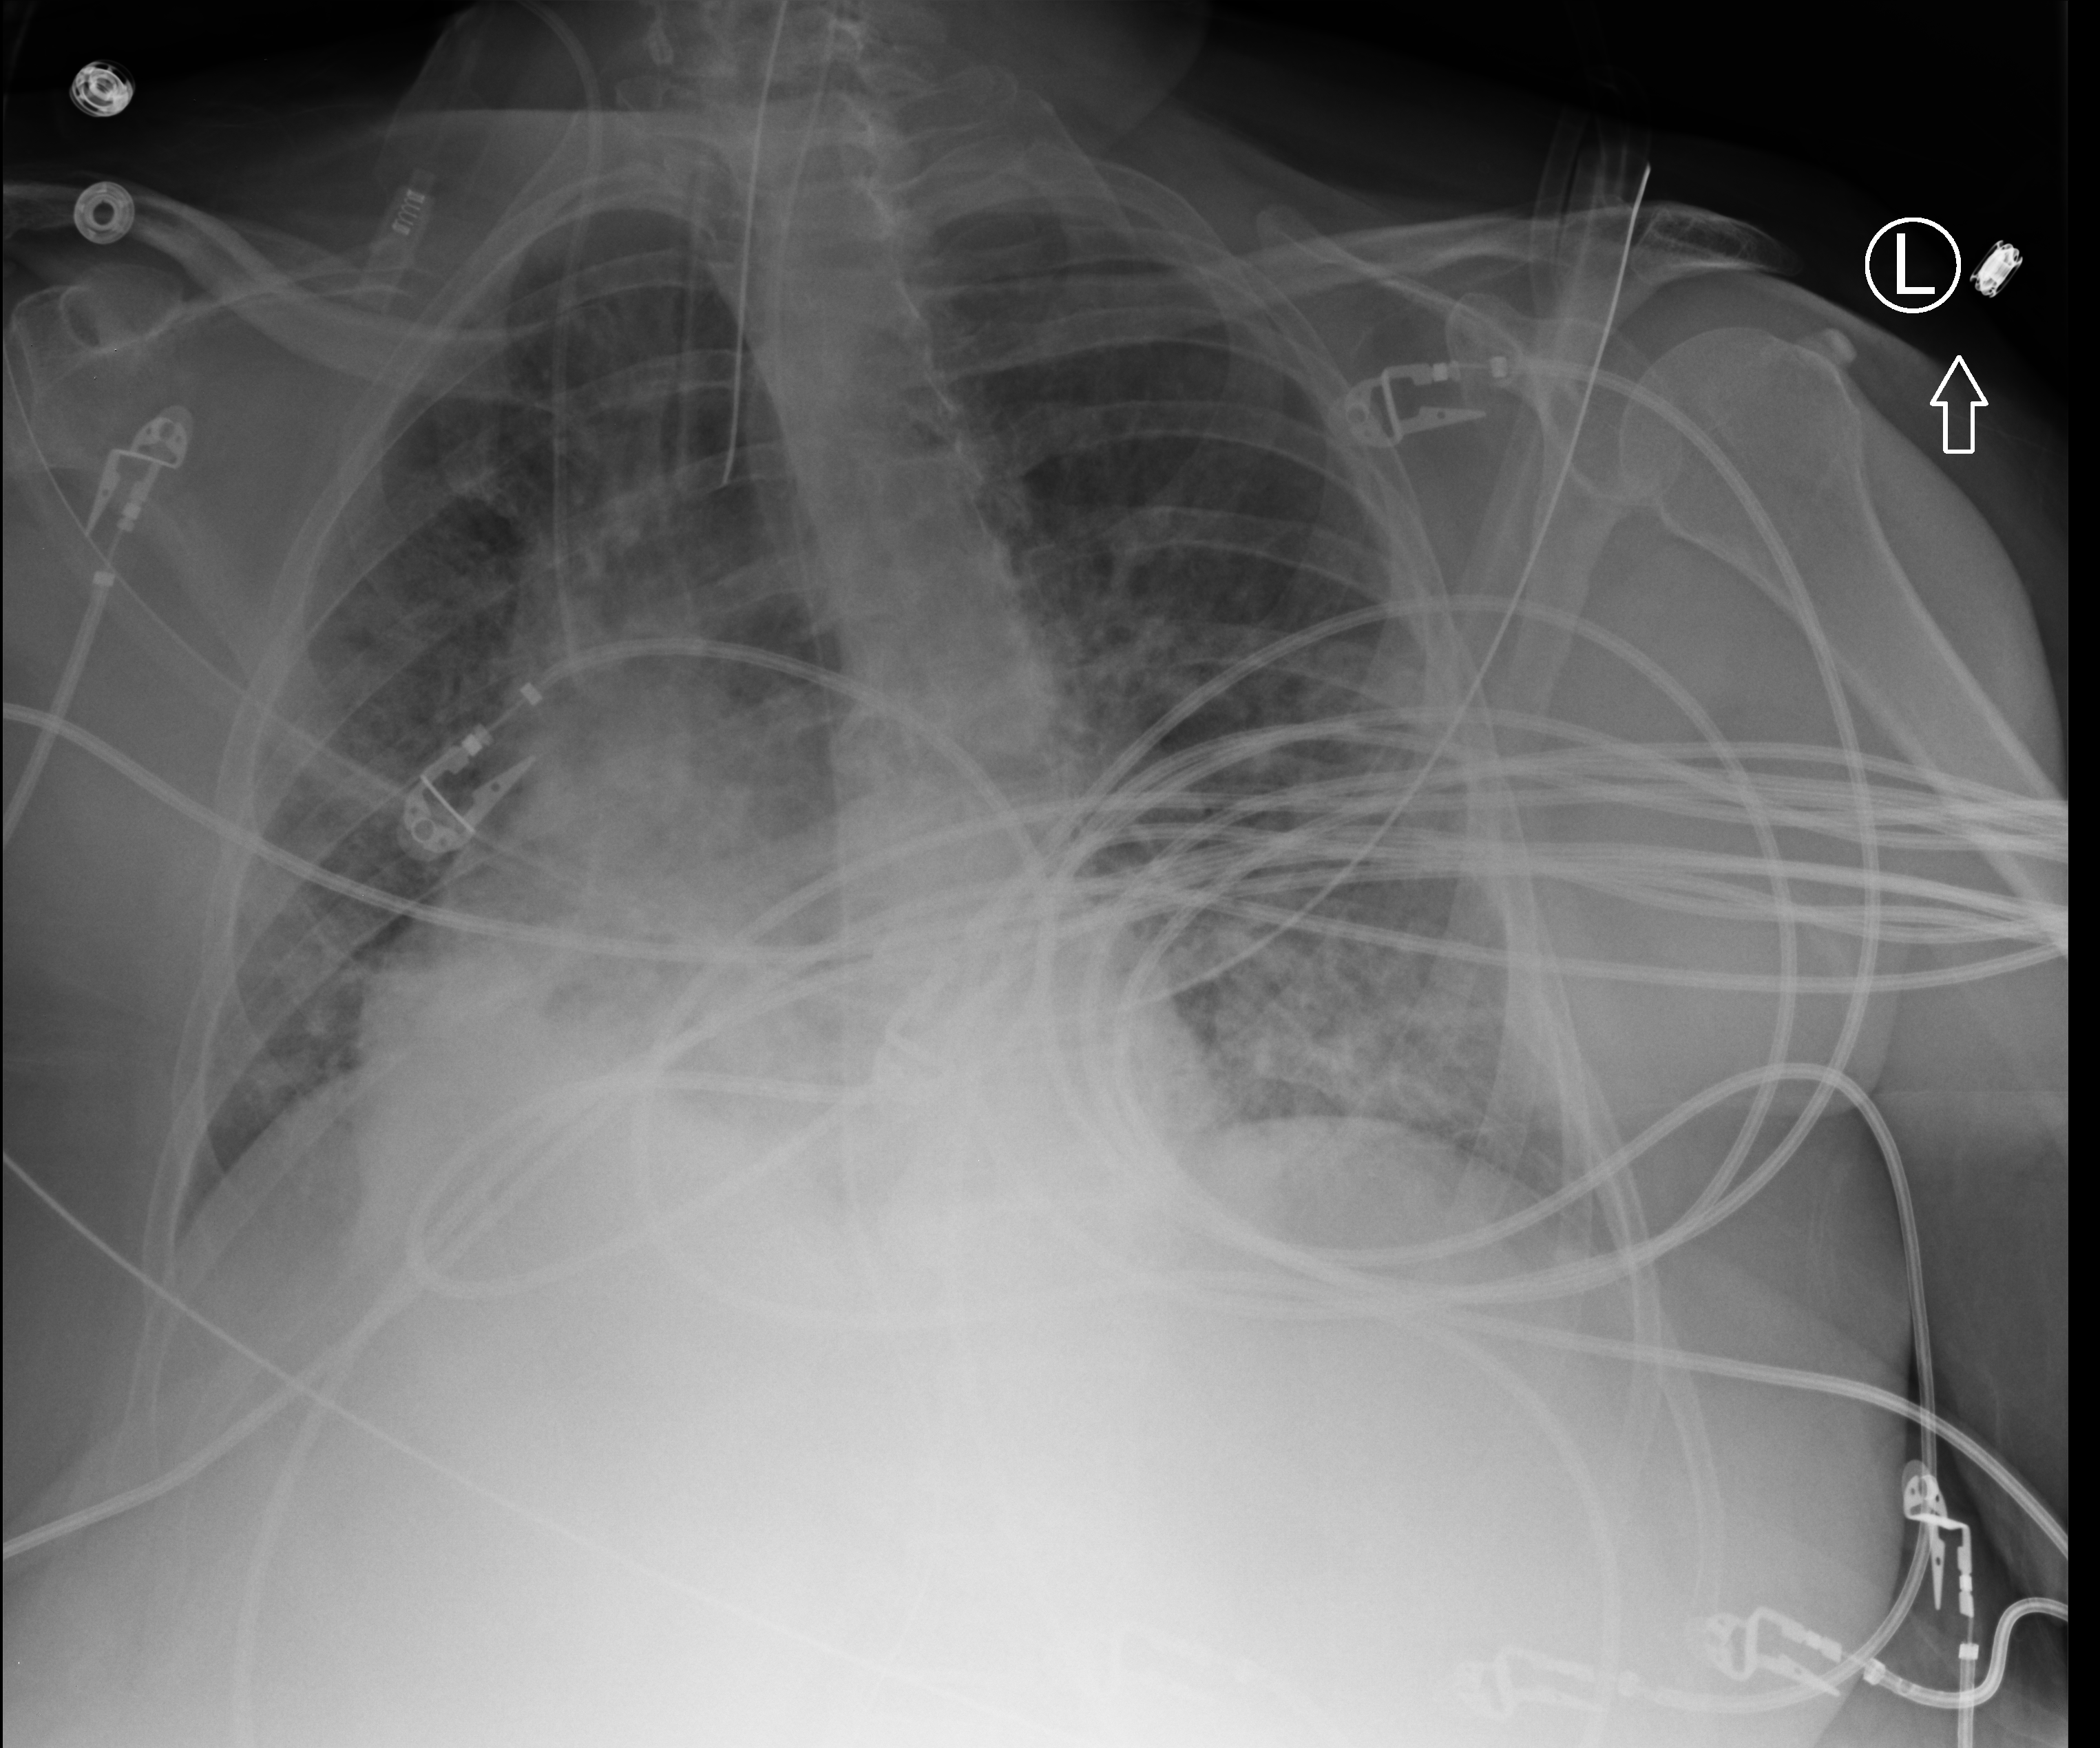
Chest X-ray (portable), anteroposterior (AP) projection. Patient hospitalised with COVID-19; female, aged 75–90 years.
From the hospital-stay record, not from the radiograph (when in the stay this image was taken is not recorded): mechanically ventilated during this hospital stay: yes.